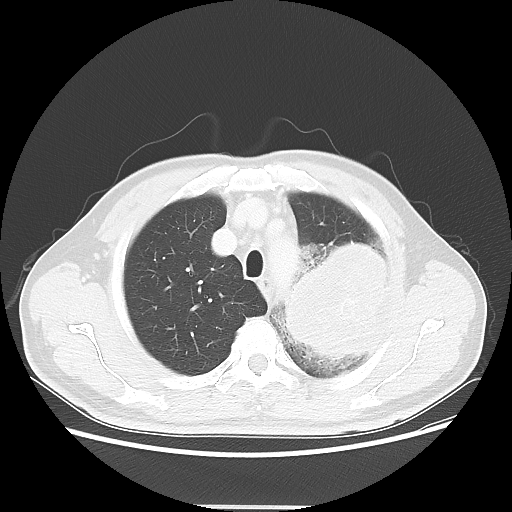
Chest CT, one axial slice. Position 44 of 53 along the scan axis. Reconstruction kernel LUNG. 100 kVp. Lung window (W 1500 / L -600 HU). 5 mm slice thickness. 512 × 512 image matrix, field of view 391 × 391 mm. Male patient, age 60 years. From the clinical record (not read from this slice): clinical TNM (as recorded): T4 N1 M1a.
Annotated regions visible in this slice (rectangle marked by the reading radiologist):
- lung tumour (recorded histology: large cell carcinoma): bounding box <265,236,392,371> (left, top, right, bottom; pixels)